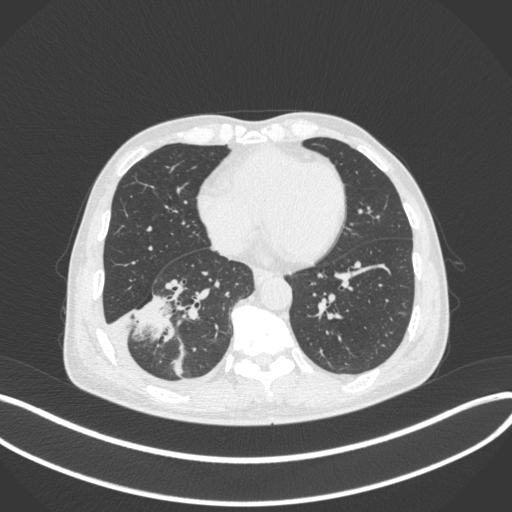
Chest CT, one axial slice; slice 138 of 385 in the series (ordered by position); reconstruction kernel B31f; 120 kVp; lung window (W 1500 / L -600 HU); 512 × 512 image matrix. Male patient, age 64 years. Case-level facts recorded for this patient, not image findings: clinical TNM (as recorded): T3 N0 M0; histopathological grade: G2-3.
Annotated regions visible in this slice (rectangle marked by the reading radiologist):
- lung tumour (recorded histology: adenocarcinoma): bounding box [x1, y1, x2, y2] px = [129, 293, 174, 346]